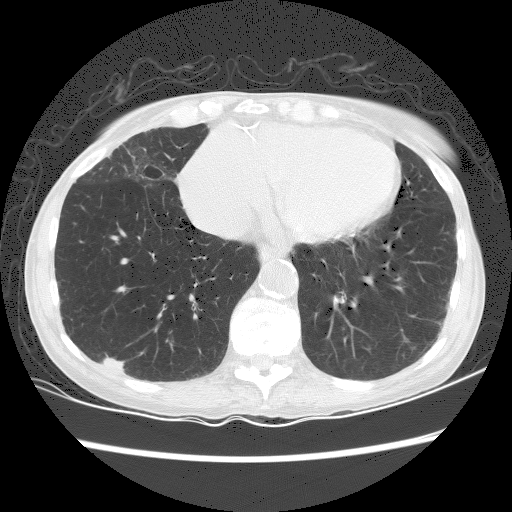
Low-dose screening chest CT, one axial slice. Position 60 of 156 along the scan axis. Reconstruction kernel BONE. Lung window (W 1500 / L -600 HU). 2.5 mm slice thickness. 512 × 512 image matrix, field of view 320 × 320 mm.
Structures marked on this image (expert manual segmentation):
- lesion 1 (tumor, lower lobe of right lung): bounding box [x1, y1, x2, y2] px = [103, 354, 125, 372]